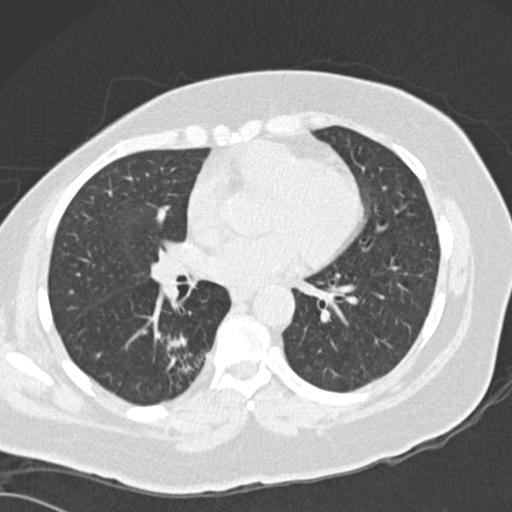
Low-dose screening chest CT, one axial slice. Reconstruction kernel B30f. 120 kVp. Lung window (W 1500 / L -600 HU). 2 mm slice thickness. 512 × 512 image matrix, field of view 328 × 328 mm.
Outlined on this slice (outlined manually by an expert reader):
- lesion 1 (tumor, lower lobe of right lung): bounding box <167,334,187,351> (left, top, right, bottom; pixels)